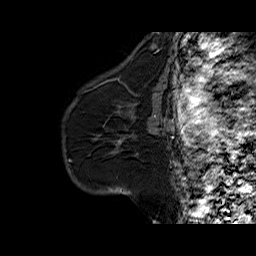
Breast MRI (dynamic contrast-enhanced), one sagittal slice. Position 44 of 60 along the scan axis. Dynamic contrast-enhanced series, time point 2 of 6 at this slice position (early post-contrast). 1.5 T. TE 6.3 ms, TR 32.5 ms. 4 mm slice thickness. 256 × 256 image matrix. Female patient. Case-level facts recorded for this patient, not image findings: setting: breast cancer imaged before/during neoadjuvant chemotherapy; receptor status: HR-positive, HER2-negative.
Structures marked on this image (semi-automatic segmentation, software-assisted and operator-edited):
- analysis volume of interest (the breast-tissue region the enhancement analysis was run in; not a lesion): bounding box <94,103,161,157> (left, top, right, bottom; pixels)
- tumour enhancement mask (voxels above the 100 % enhancement threshold inside the analysis volume of interest): <154,115,156,117>